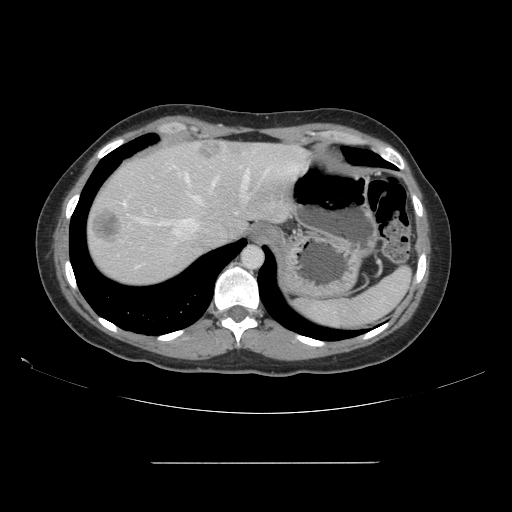
Contrast-enhanced abdominal CT, one axial slice. Slice 127 of 151 in the series (ordered by position). Intravenous contrast given. Soft-tissue window (W 400 / L 40 HU). 512 × 512 image matrix, field of view 421 × 421 mm. Female patient, age 46 years. Case-level facts recorded for this patient, not image findings: diagnosis: colorectal cancer liver metastases, imaged before liver resection; multiple liver metastases: yes; largest metastasis: 3 cm; disease in both lobes: yes.
Annotated regions visible in this slice (outlined manually by an expert reader):
- hepatic veins: bounding box [x1, y1, x2, y2] px = [123, 152, 254, 237]
- liver: [87, 141, 302, 285]
- planned liver remnant (the part of the liver to remain after resection): [98, 143, 303, 243]
- liver metastasis: [93, 212, 122, 244]
- liver metastasis: [200, 145, 224, 160]